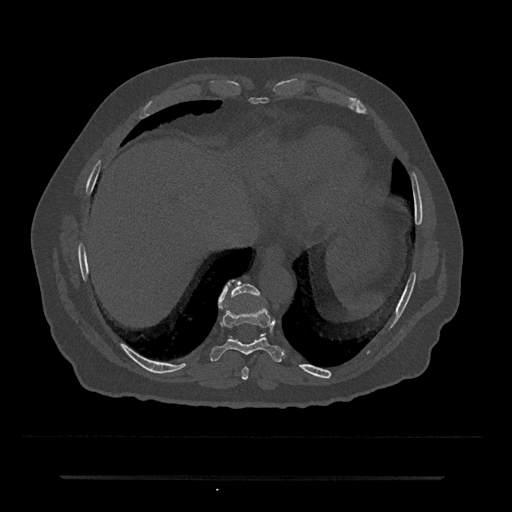
CT including the spine, one axial slice; position 273 of 797 along the scan axis; 120 kVp; bone window (W 1800 / L 400 HU); 0.5 mm slice thickness; 512 × 512 image matrix. Male patient, age 69 years. From the clinical record (not read from this slice): primary cancer: prostate.
Annotated regions visible in this slice (semi-automatically segmented with operator editing):
- T10 vertebra: bounding box (x1, y1, x2, y2) in pixels: (219, 280, 265, 335)
- T8 vertebra: (241, 367, 249, 380)
- T9 vertebra: (210, 280, 285, 362)